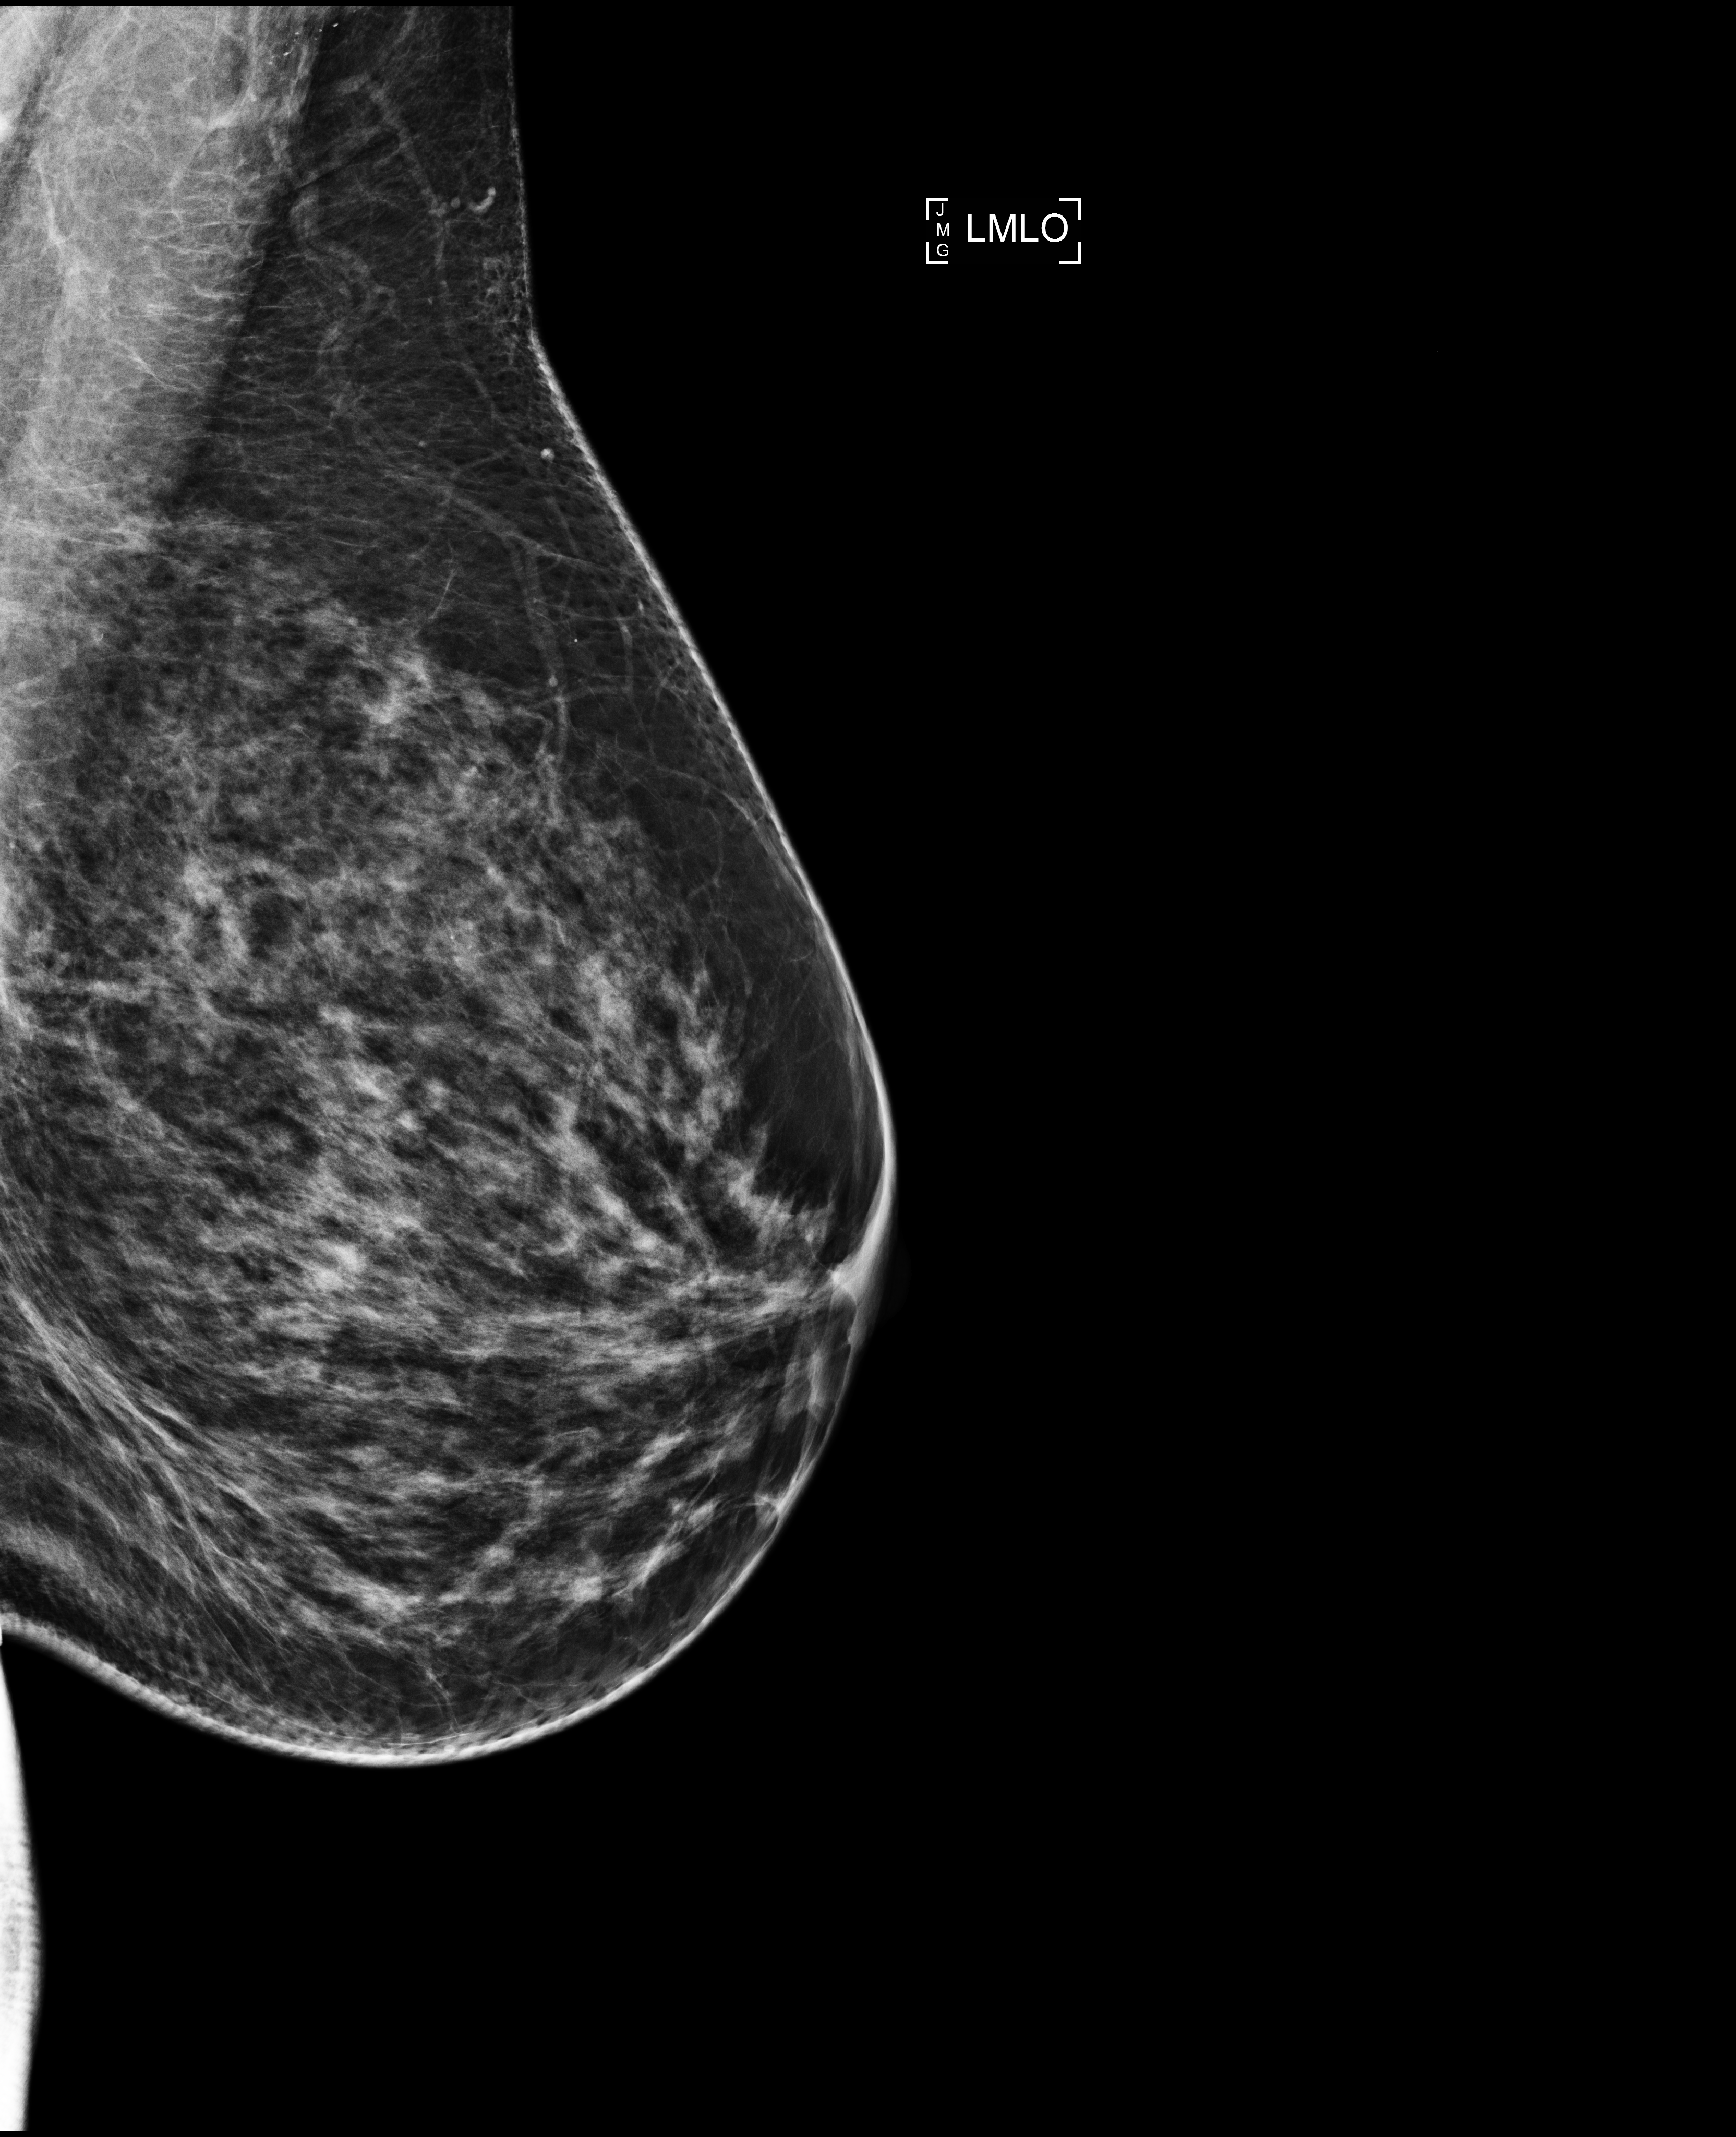
Annual screening mammography examination; compressed breast thickness 70 mm. Patient aged 55 years (female).
Image type: full-field digital mammogram. Breast: left. Projection: medio-lateral oblique projection. Breast density at the screening exam (both breasts): heterogeneously dense (BI-RADS density category c). Final BI-RADS category for the screening round (tomosynthesis exam, both breasts): category 1. Recall: no recall after this screen.